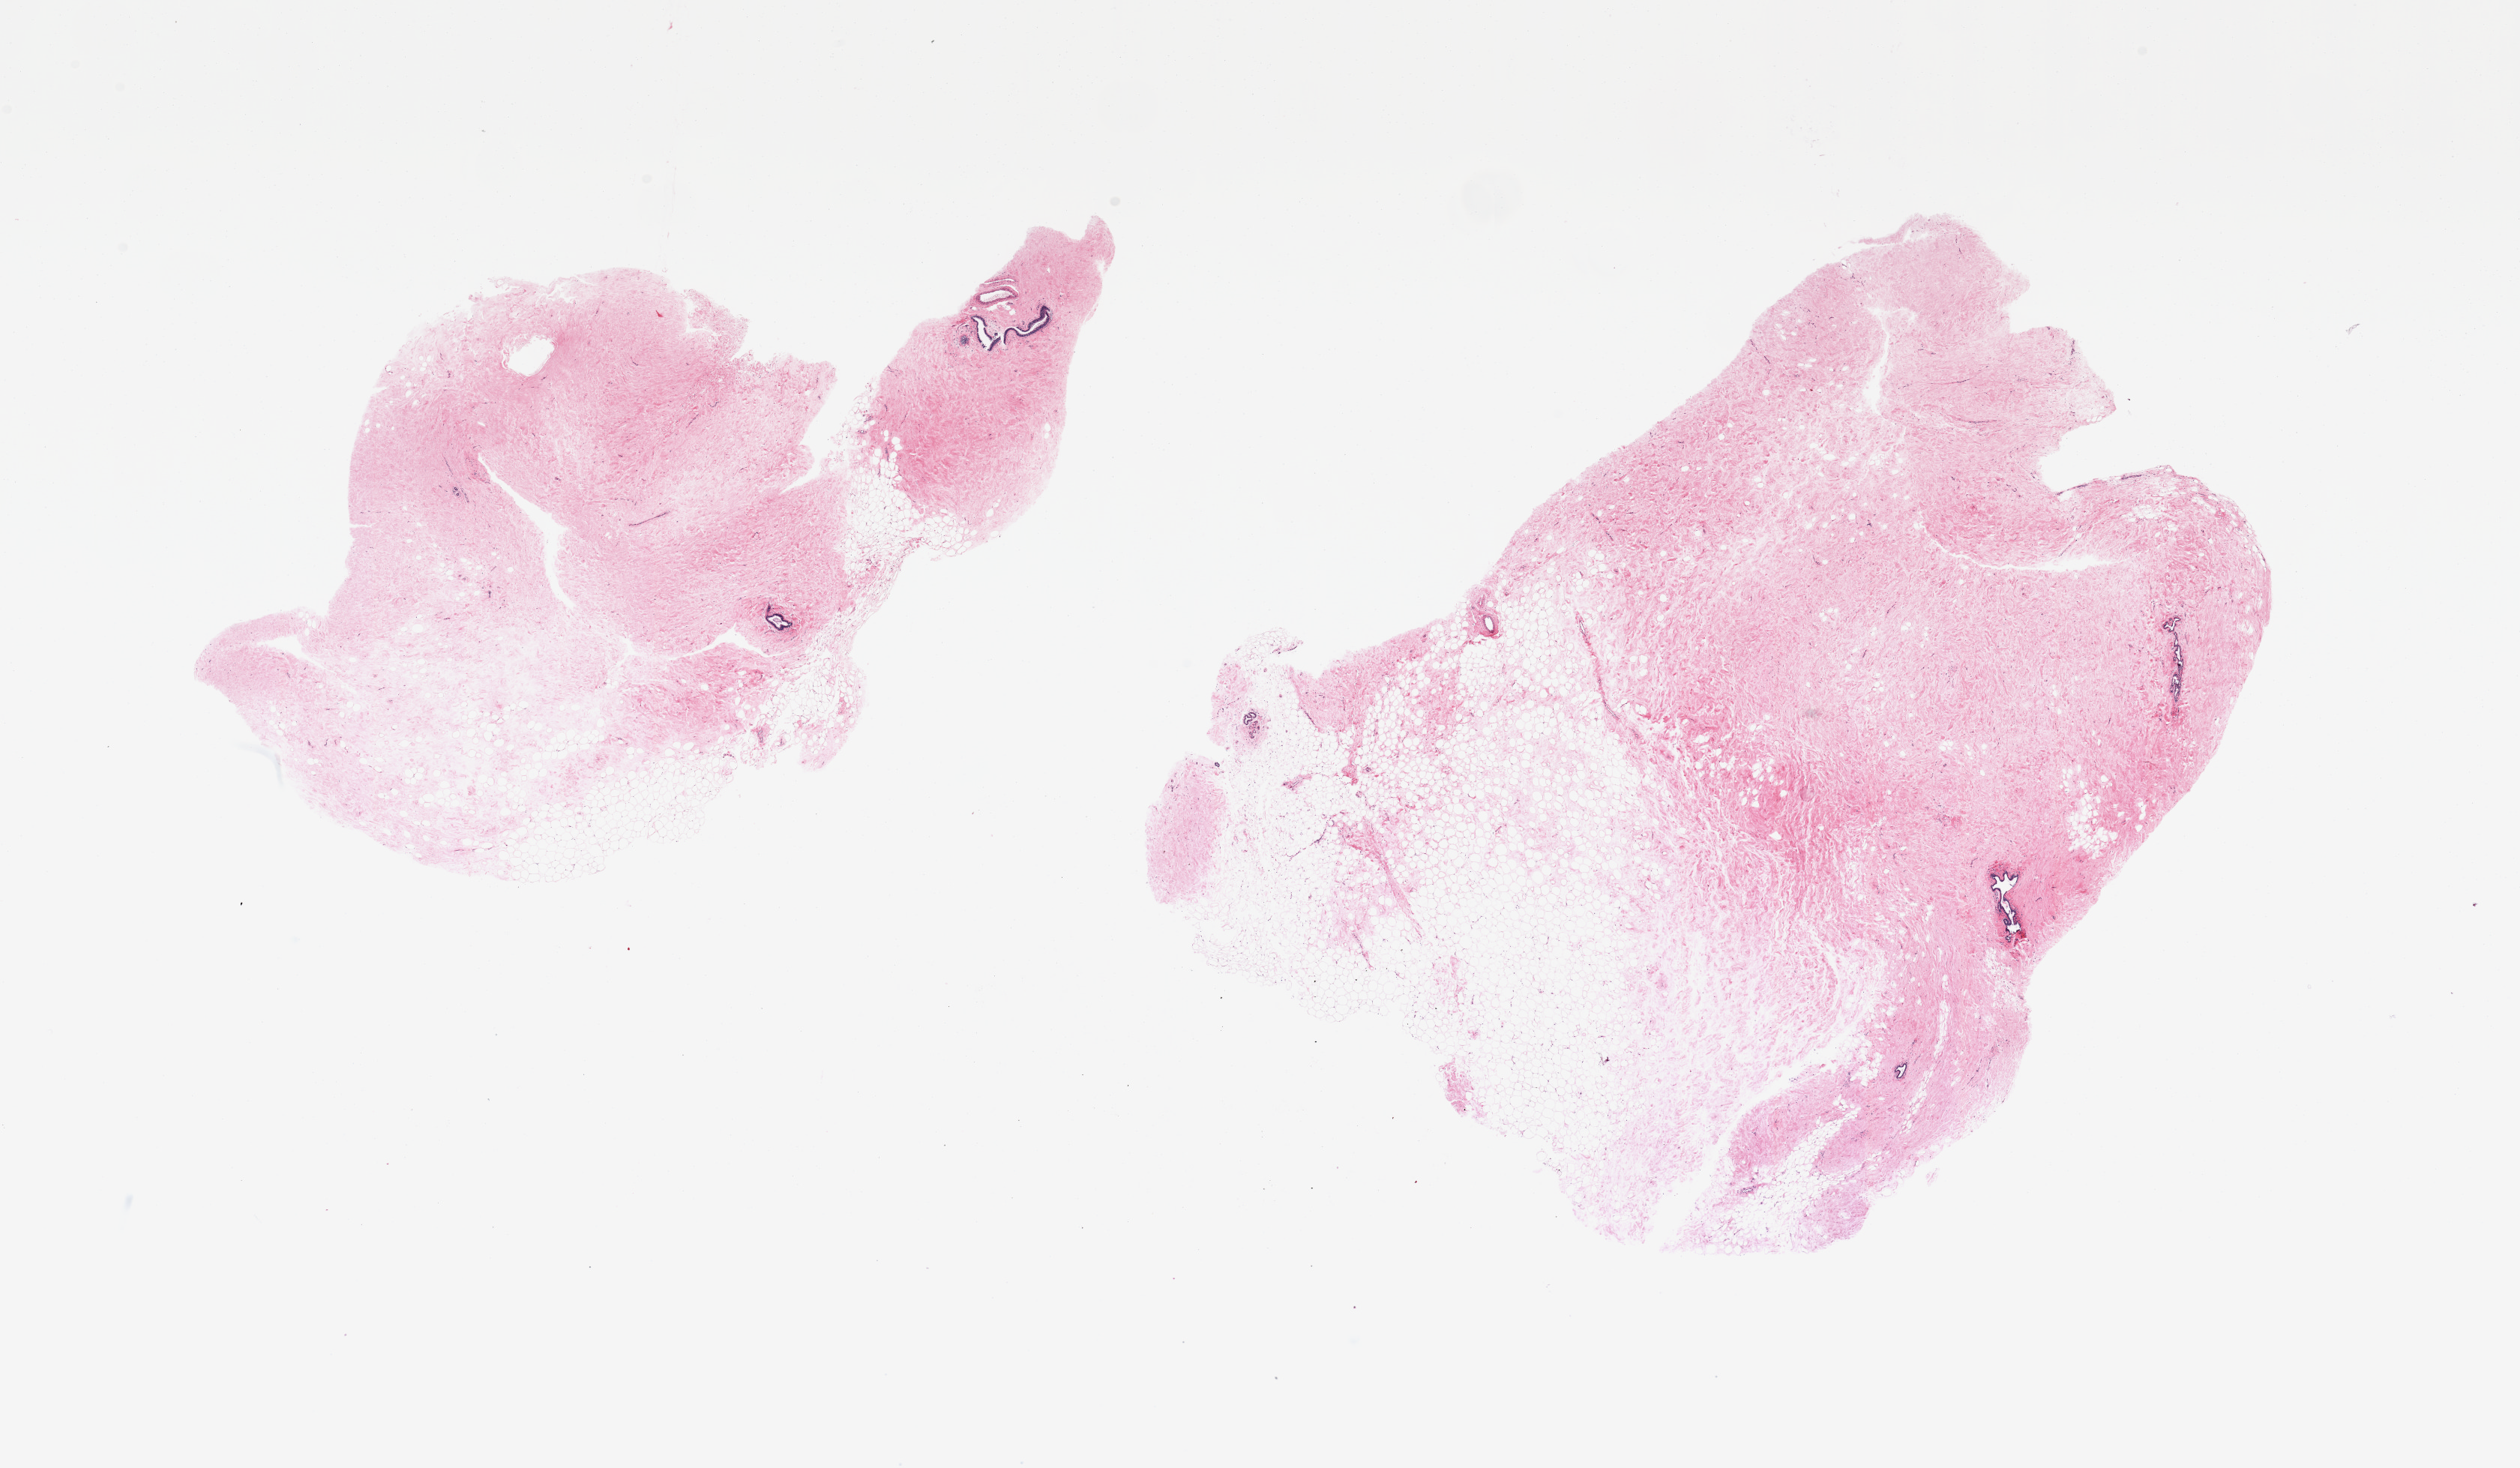
H&E whole-slide image — shown as a low-resolution overview of the whole scanned area (about 26.6 x 15.5 mm, from a 20x scan); PAXgene-fixed paraffin-embedded (PFPE) section; sampled site (target tissue): breast; donor tissue sample. Donor: female.
Reviewer comment on this tissue sample: 2 pieces; 20-30% fat, remainder is fibrocollagenous tissue with rare ducts, focus of microcalcification.